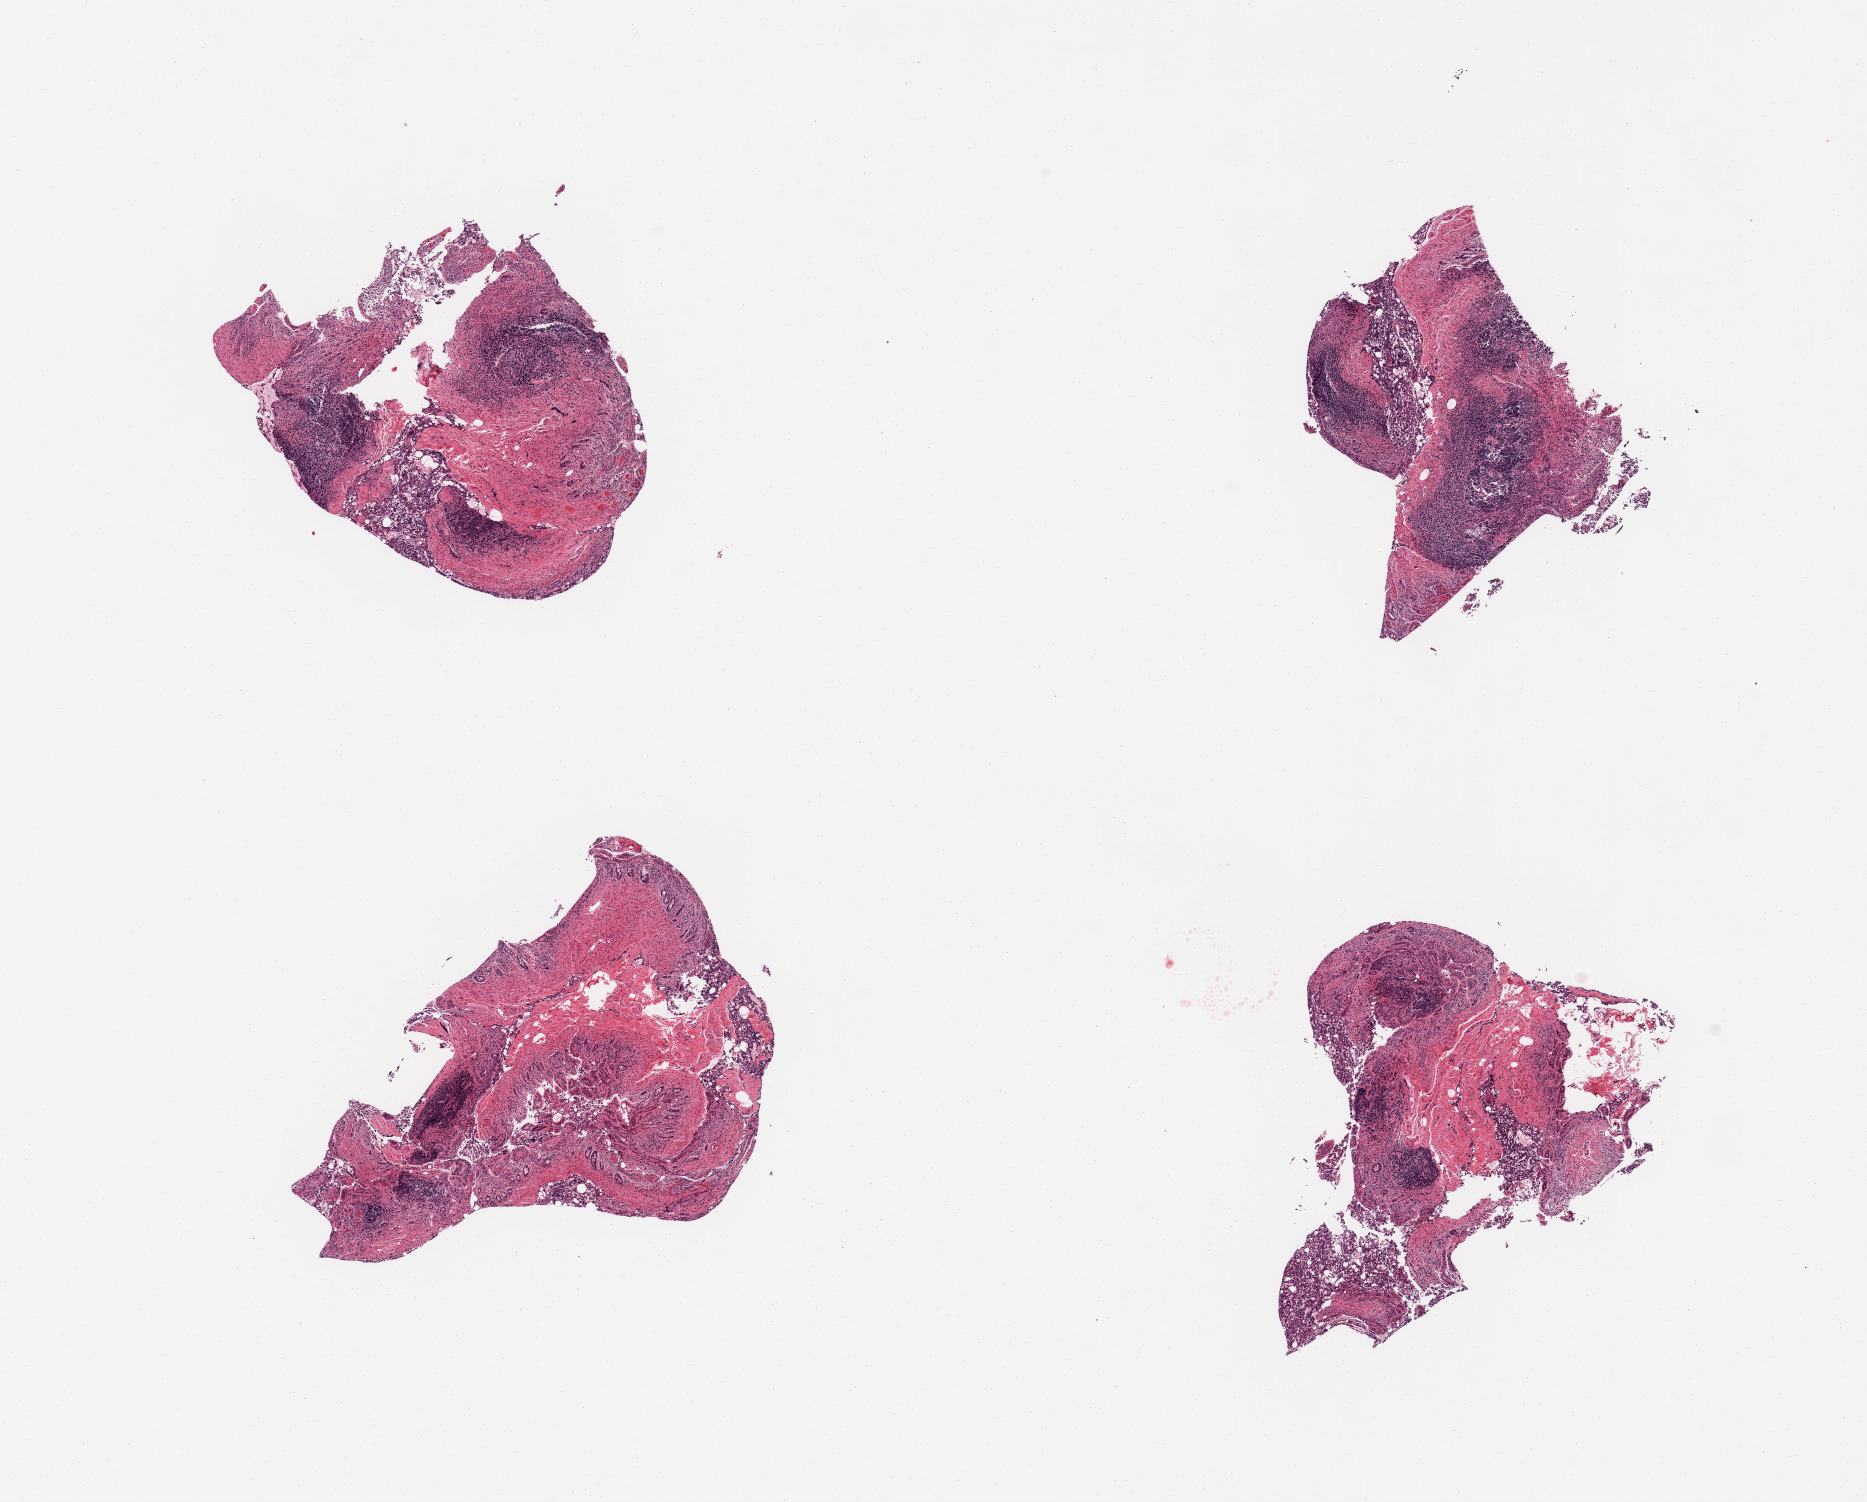
Digitized H&E-stained section — whole scanned area (about 14.8 x 11.9 mm, from a 20x scan) shown as a low-resolution overview, PAXgene-fixed paraffin-embedded (PFPE) section, section of ileum (target tissue), tissue donor sample. Donor: male.
Review note (as recorded): 4 pieces, glands autolyzed; residual target lymphoid aggregates are ~20% of tissue.